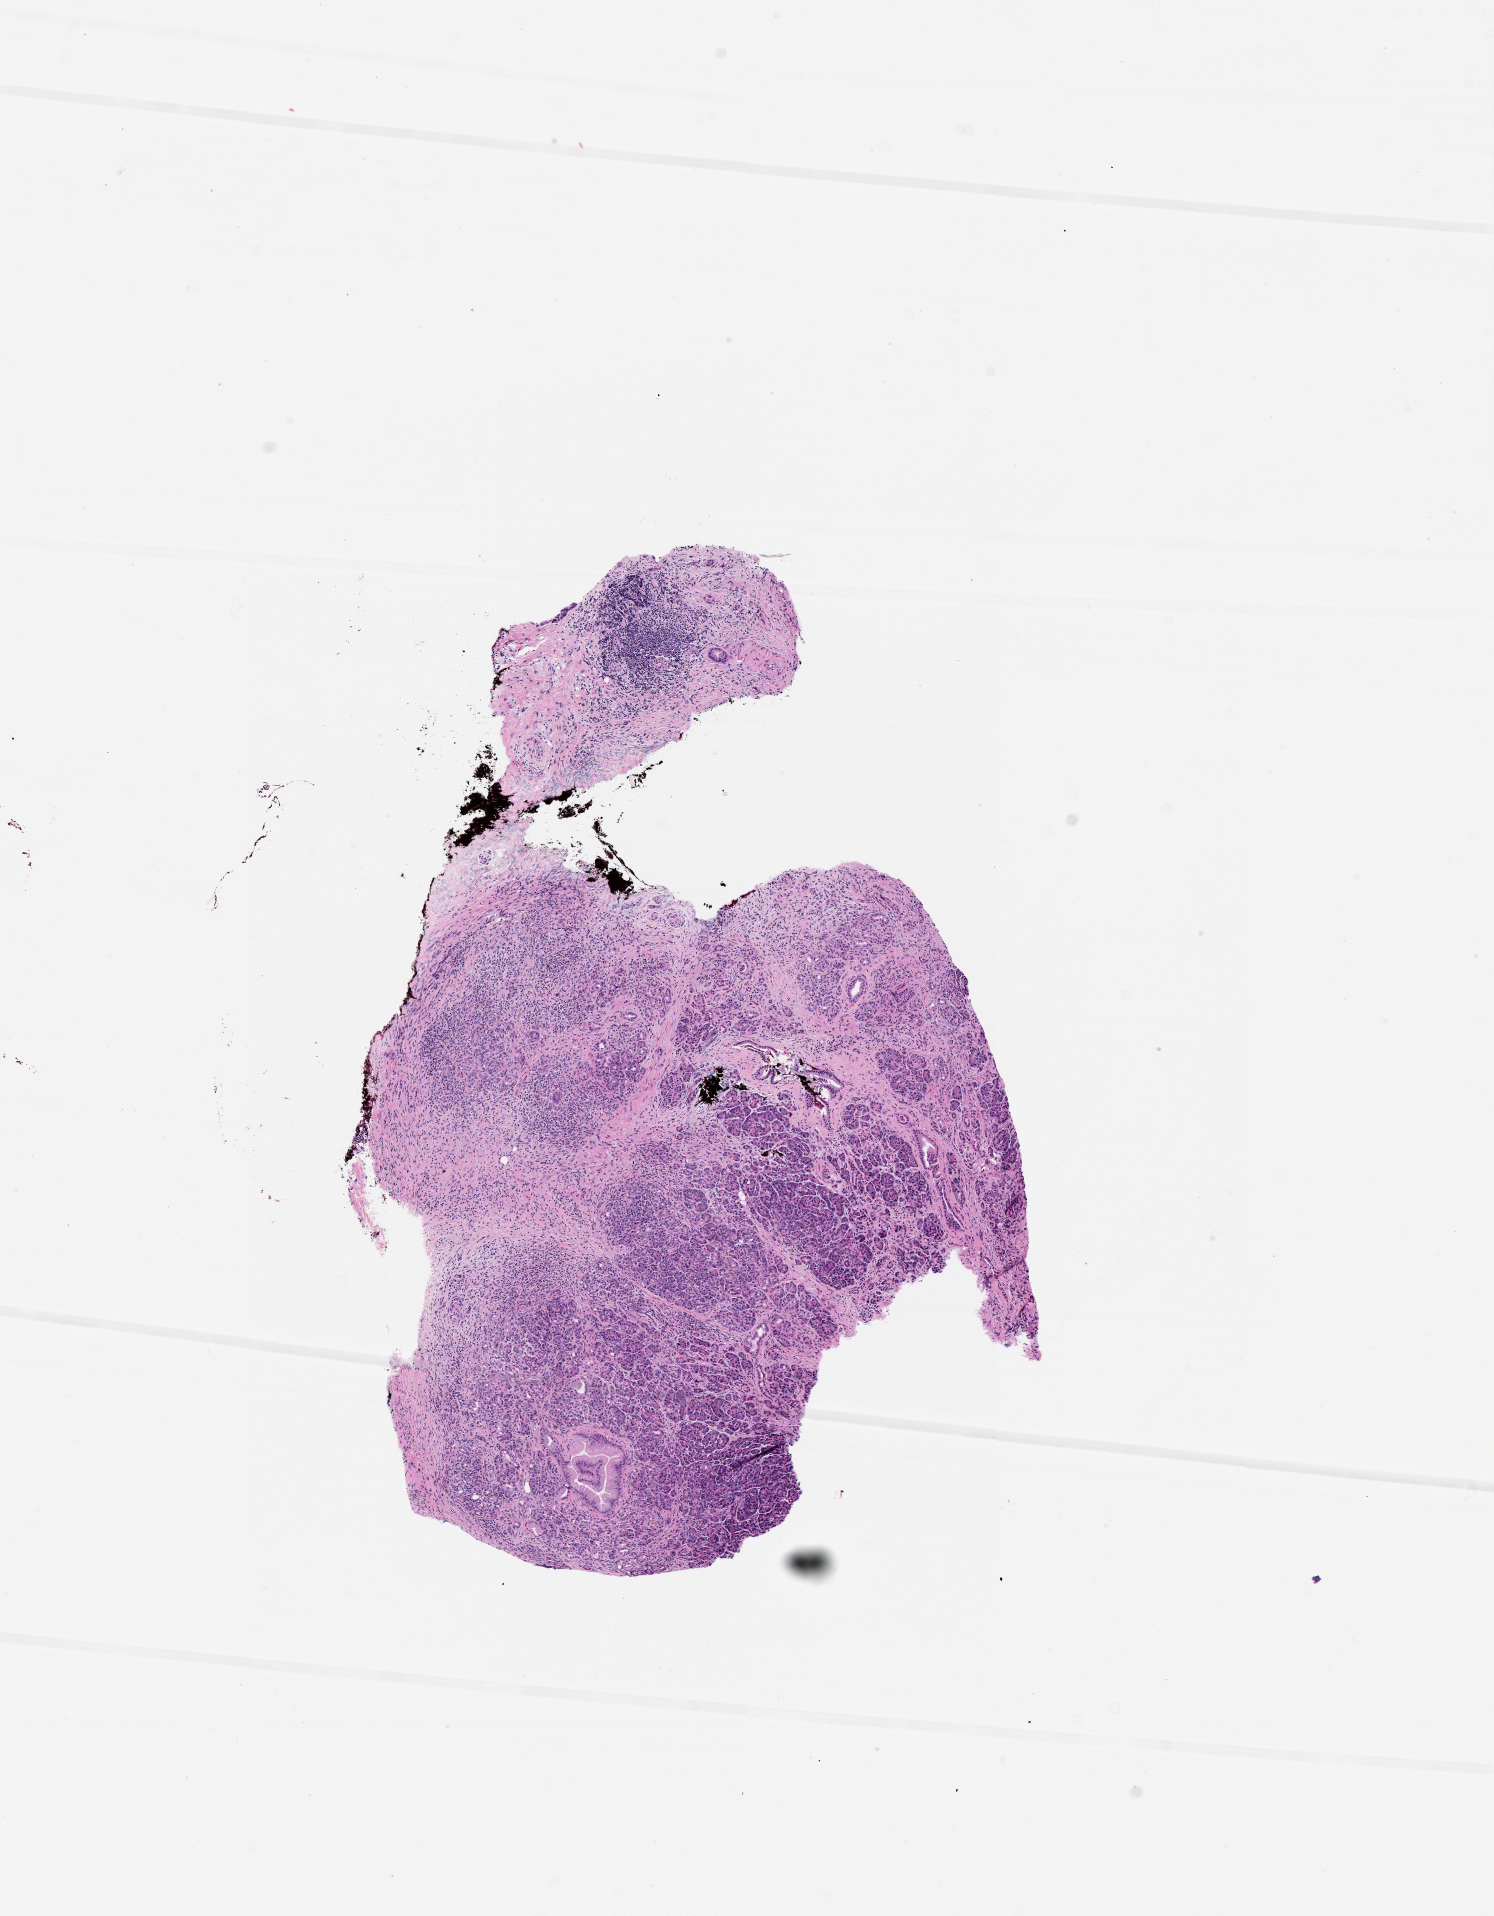
Digitized Hematoxylin and eosin (H&E) stained tissue section (whole slide) — a low-resolution overview of the entire scanned area, about 6.0 x 7.7 mm; tumour tissue sample, sampled site: pancreas. Patient: female, age 85 years. Histologic grade: G2 (moderately differentiated). Pathologist review of this section (percent, as recorded): tumour nuclei 5%, necrosis 0%.
* histologic diagnosis: Infiltrating duct carcinoma, NOS
* AJCC pathologic stage: IIA
* primary tumour site (as recorded): head